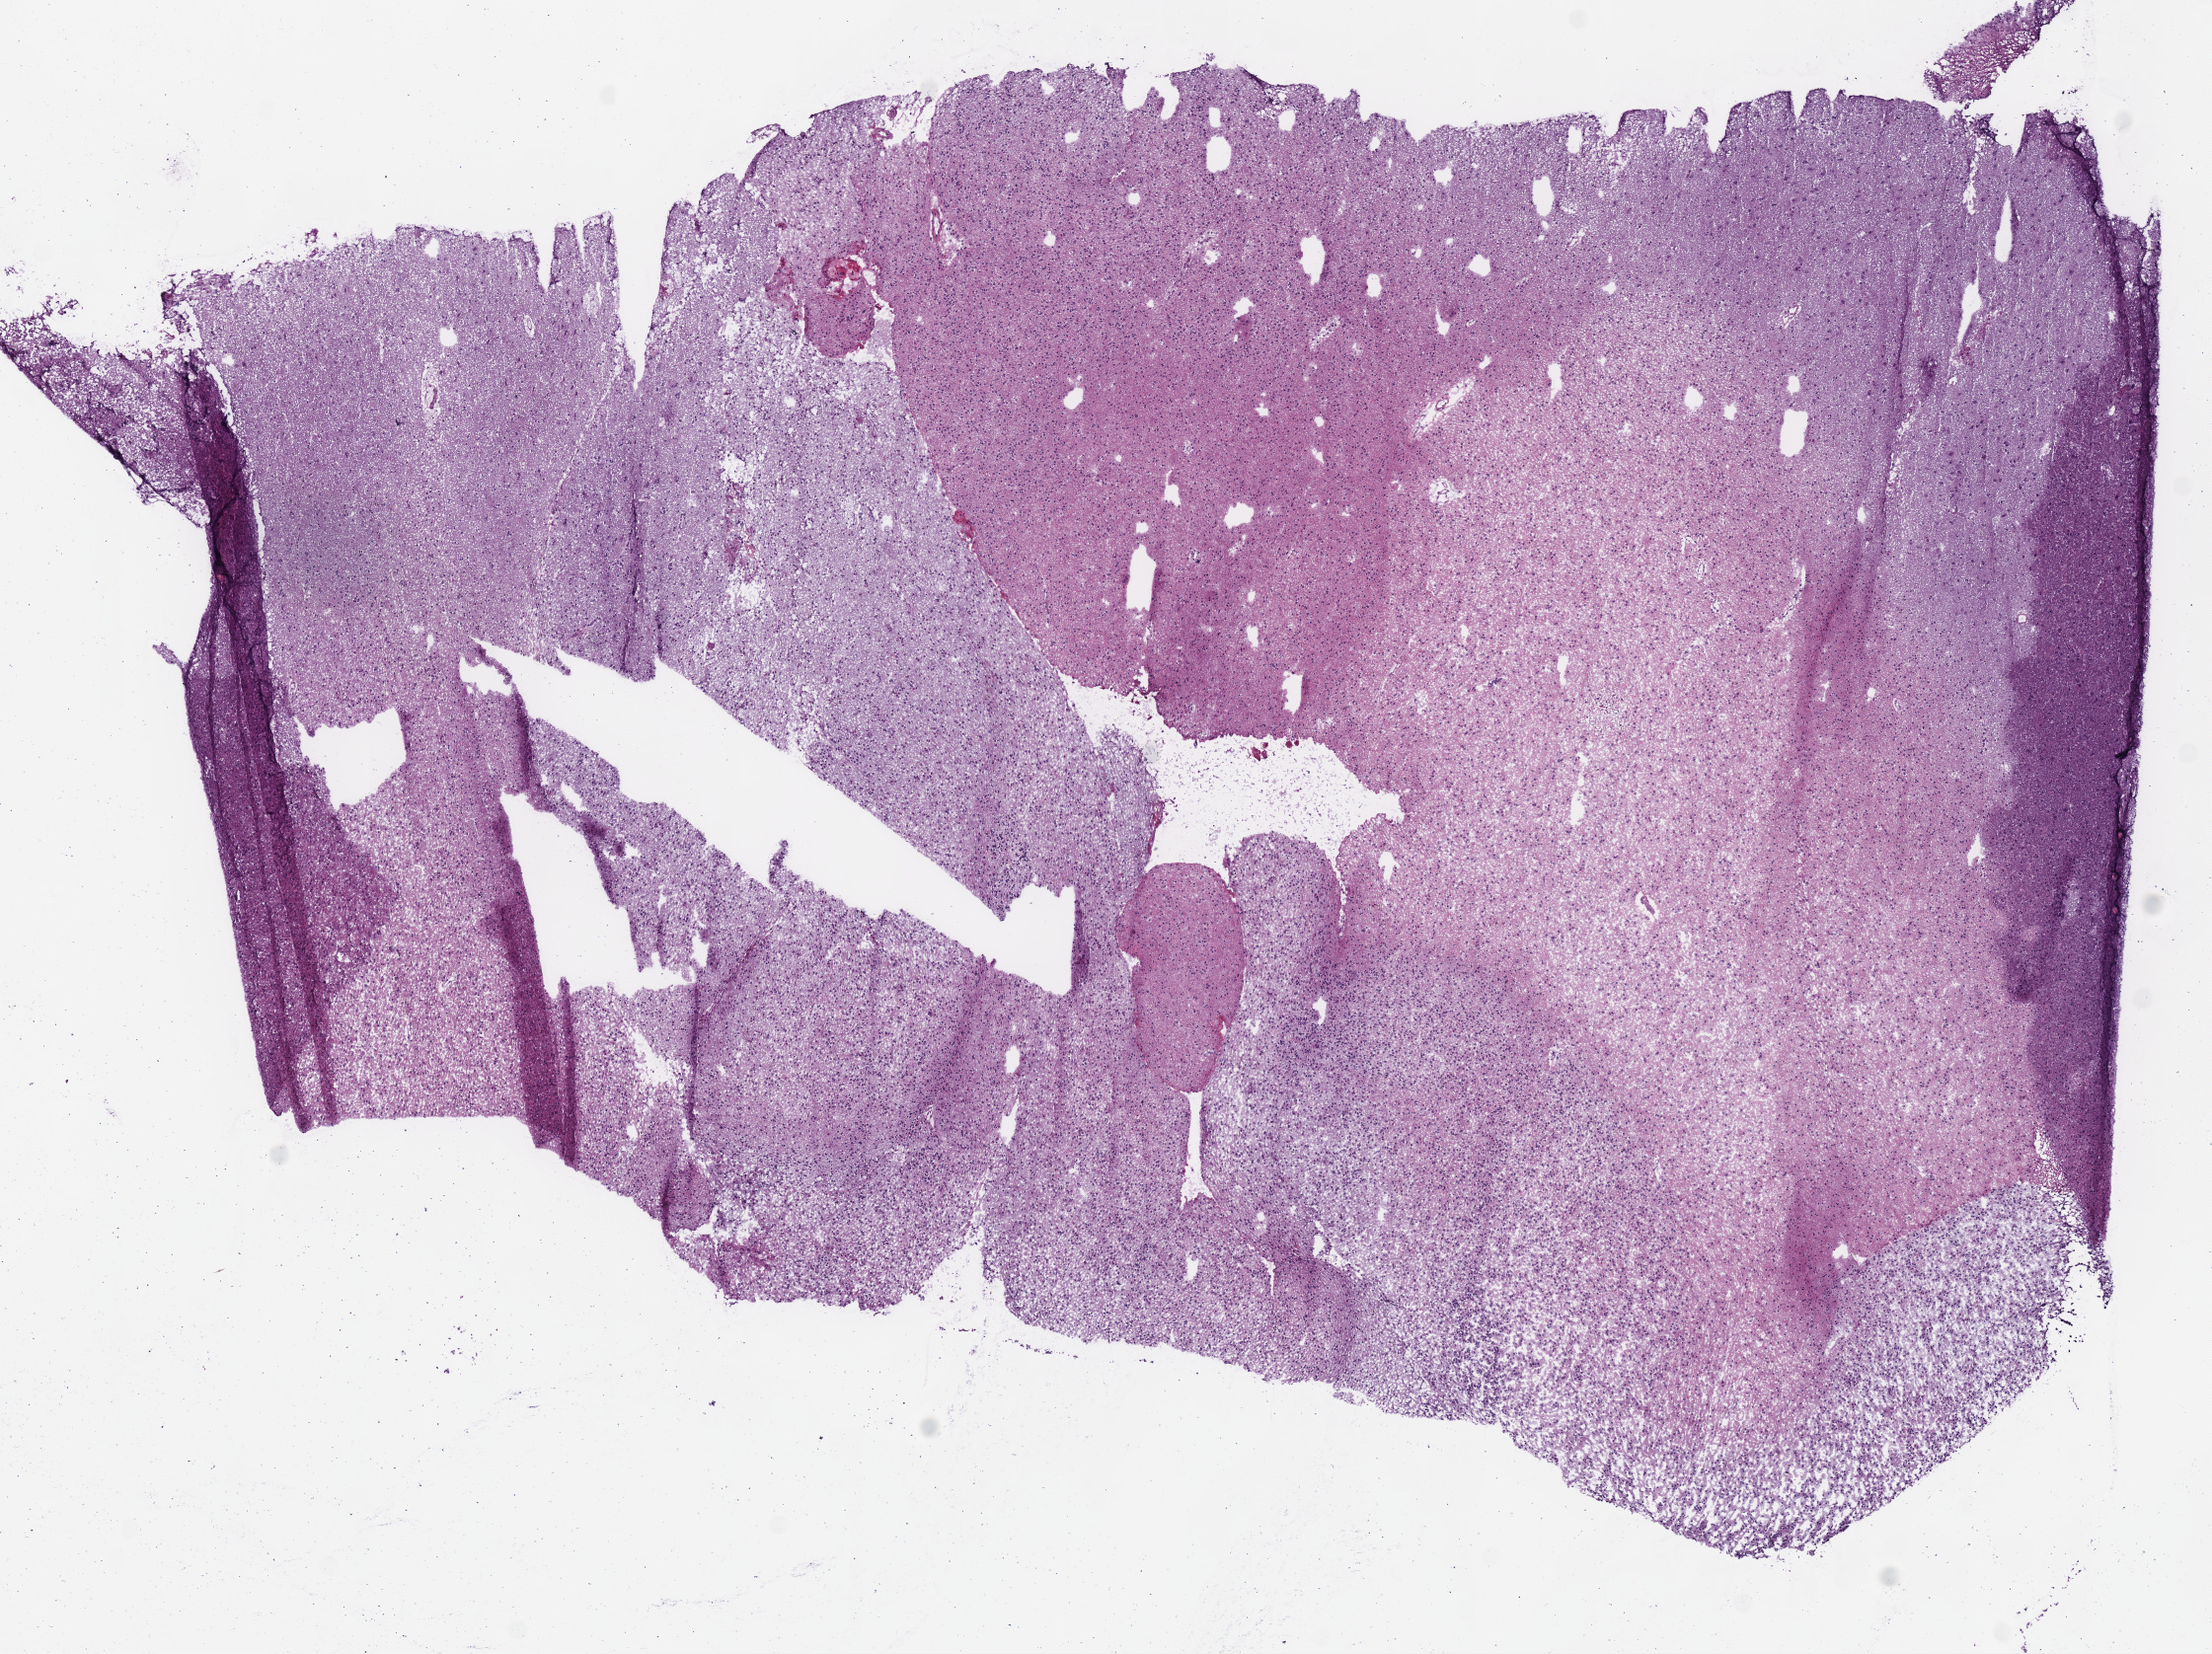
Whole-slide histology image, Hematoxylin and eosin (H&E) stained, shown as a low-resolution overview of the whole scanned area (about 8.8 x 6.6 mm), frozen section, brain, primary tumour sample. Patient: male, age at initial diagnosis 64 years. Histologic grade: G3 (poorly differentiated). Composition of this section per pathologist review: tumour cells 100%, tumour nuclei 75%, normal cells 0%, stromal cells 0%, necrosis 0%.
* laterality: right
* histologic diagnosis: Oligodendroglioma, anaplastic (cerebrum)